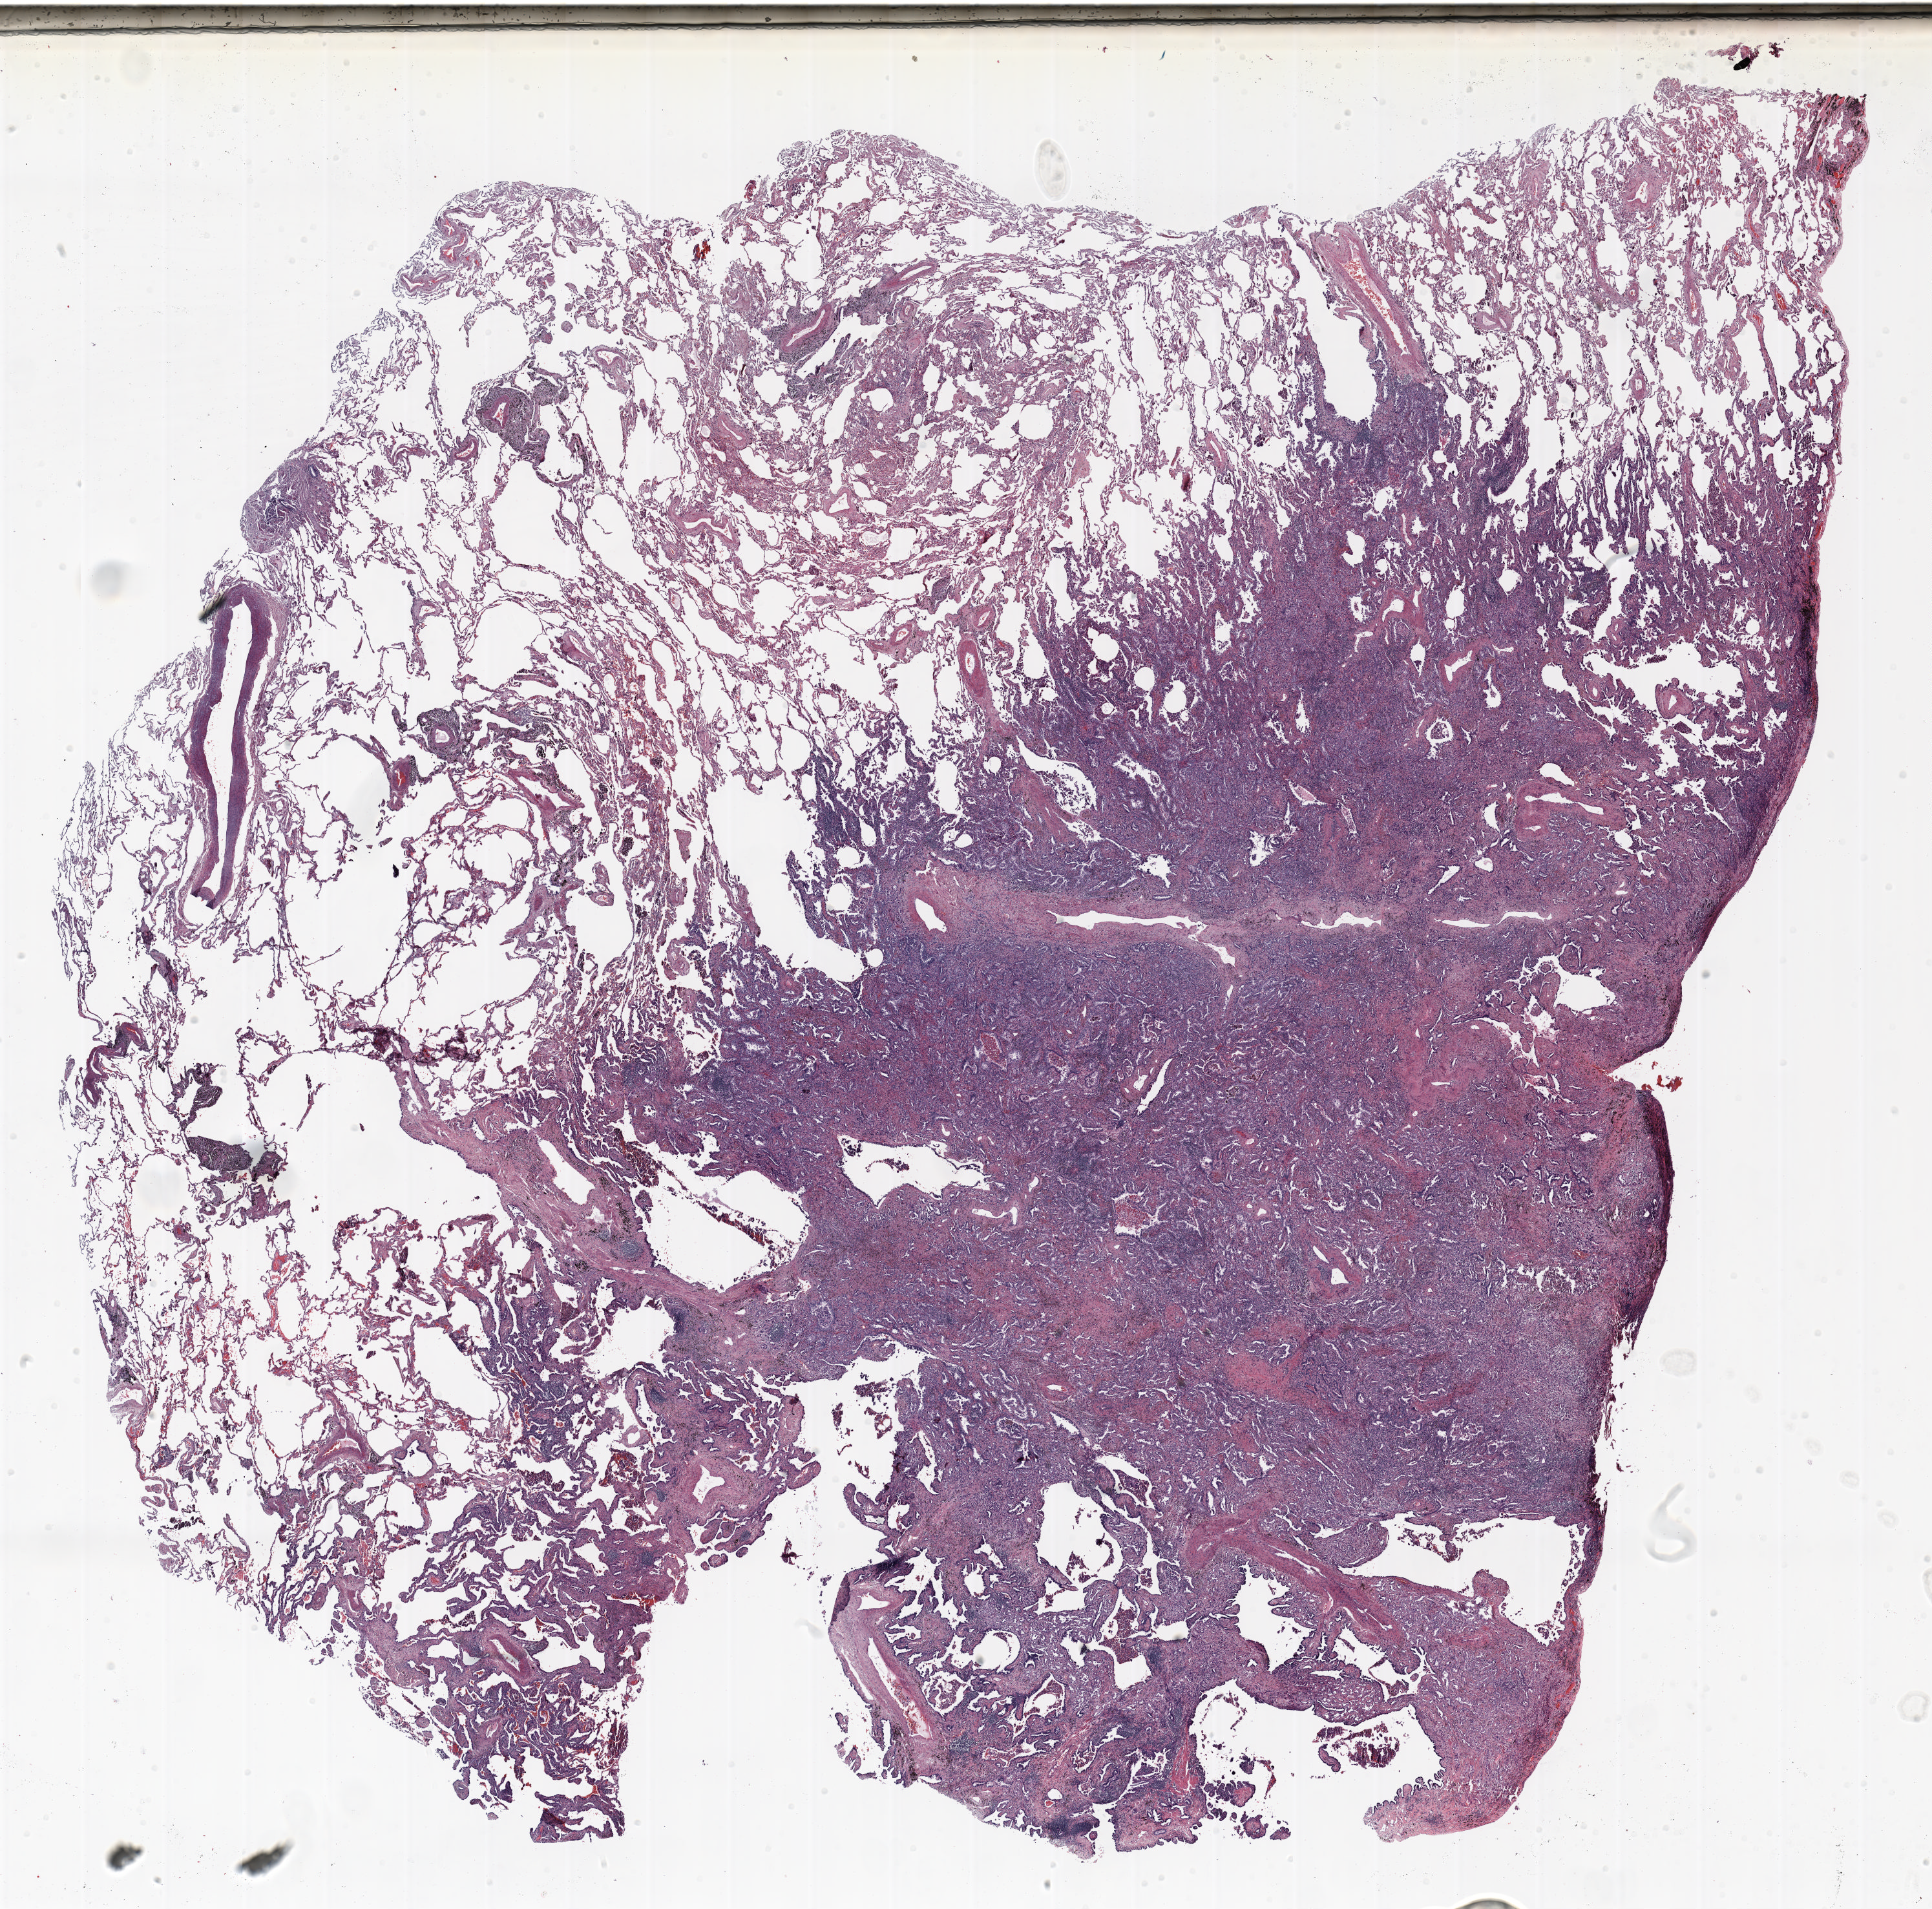
Hematoxylin and eosin (H&E) stained whole-slide image — shown as a low-resolution overview of the whole scanned area (about 24.0 x 23.7 mm); formalin-fixed paraffin-embedded (FFPE) section; lung tissue. Male patient, aged 72 at enrolment. Current smoker at enrolment. Grade: moderately differentiated (G2).
Stage (AJCC 6th edition): IB. Participant's lung-cancer diagnosis: Adenocarcinoma, NOS (ICD-O-3 8140/3). Tumour size (pathology): 30 mm. Primary tumour location (clinical record): right upper lobe. ICD-O-3 topography: upper lobe of lung (C34.1).